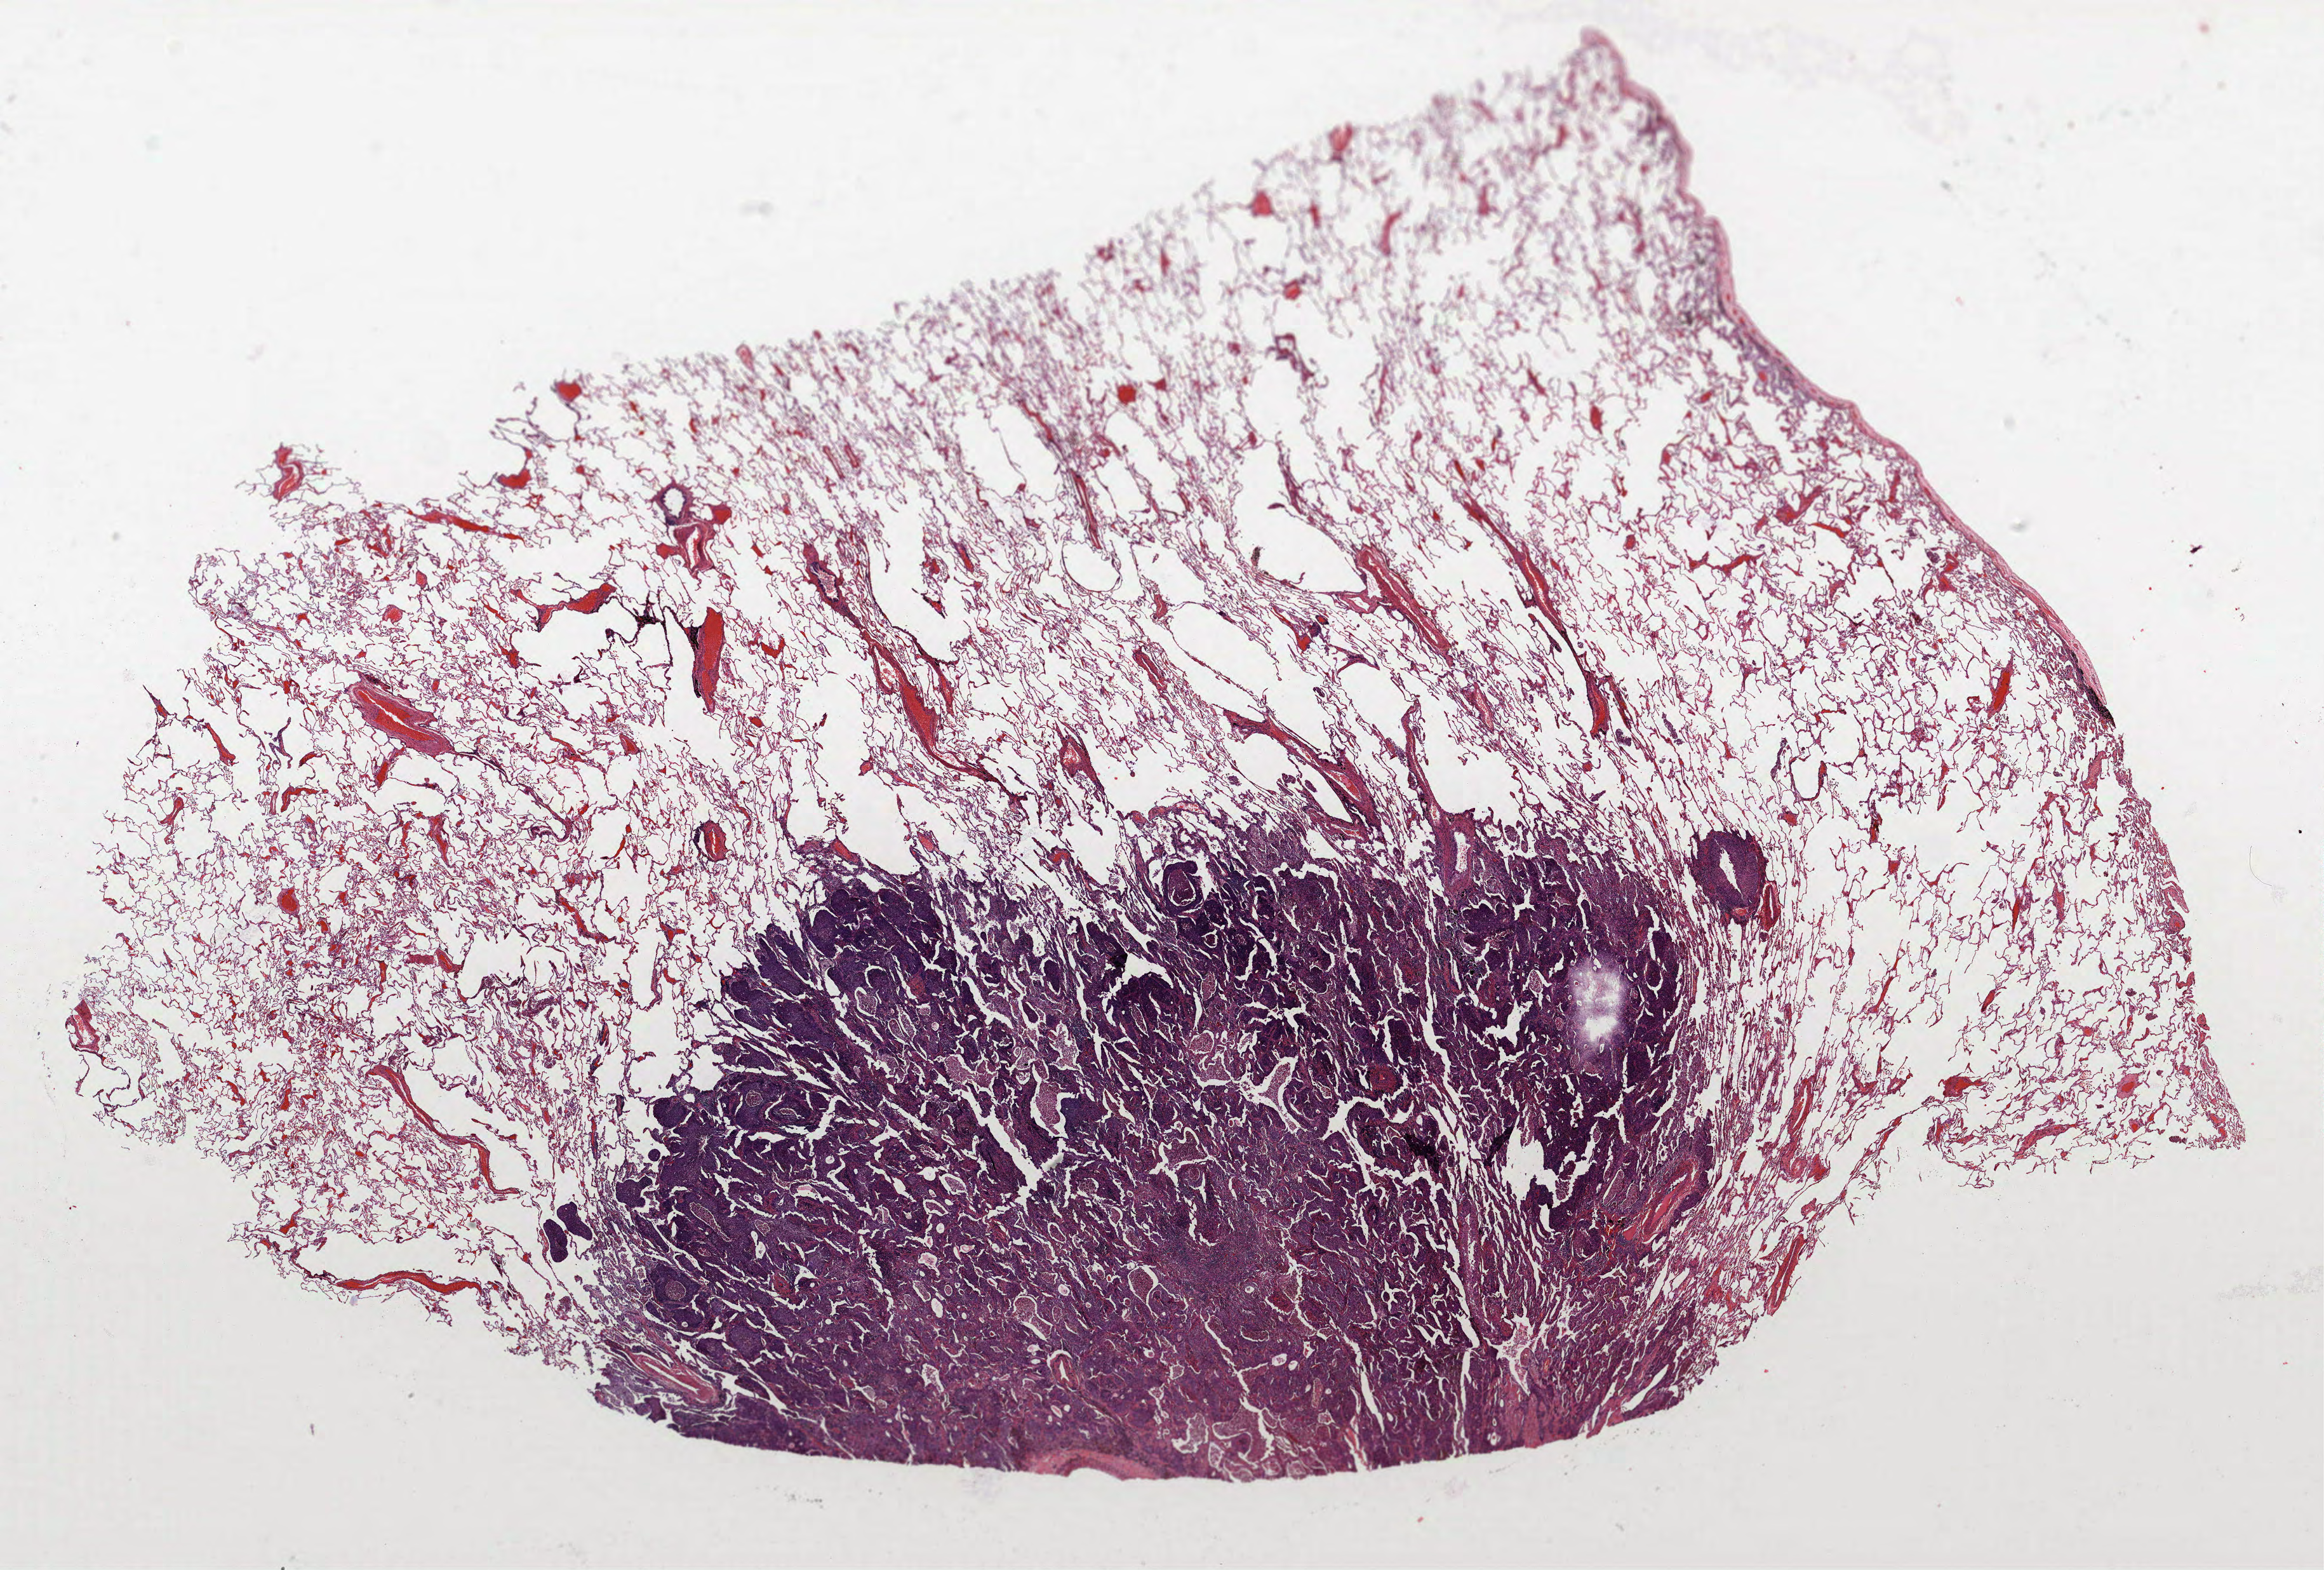
Whole-slide histology image, H&E — whole scanned area (about 29.3 x 19.8 mm) shown as a low-resolution overview. Formalin-fixed paraffin-embedded (FFPE) section. Lung tissue. Male, age 68 at enrolment. Current smoker at enrolment. Grade: moderately differentiated (G2).
Tumour size (pathology): 25 mm. ICD-O-3 topography: upper lobe of lung (C34.1). Participant's lung-cancer diagnosis: Squamous cell carcinoma, NOS (ICD-O-3 8070/3). Stage (AJCC 6th edition): IIA. Primary tumour location (clinical record): left upper lobe.